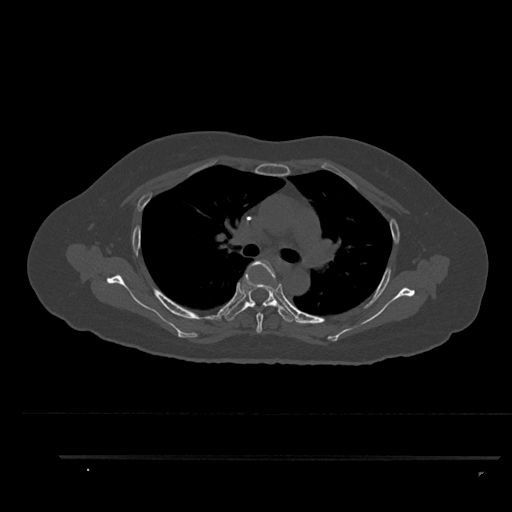
CT including the spine, one axial slice; slice 618 of 797 in the series (ordered by position); 120 kVp; bone window (W 1800 / L 400 HU); 0.5 mm slice thickness; 512 × 512 image matrix, field of view 408 × 408 mm. Patient: female, 44 years. Case-level facts recorded for this patient, not image findings: primary cancer: renal; vertebrae with lytic lesions (as recorded): L1.
Outlined on this slice (semi-automatic segmentation, software-assisted and operator-edited):
- T4 vertebra: bounding box [x1, y1, x2, y2] px = [251, 260, 278, 333]
- T5 vertebra: [223, 274, 298, 323]